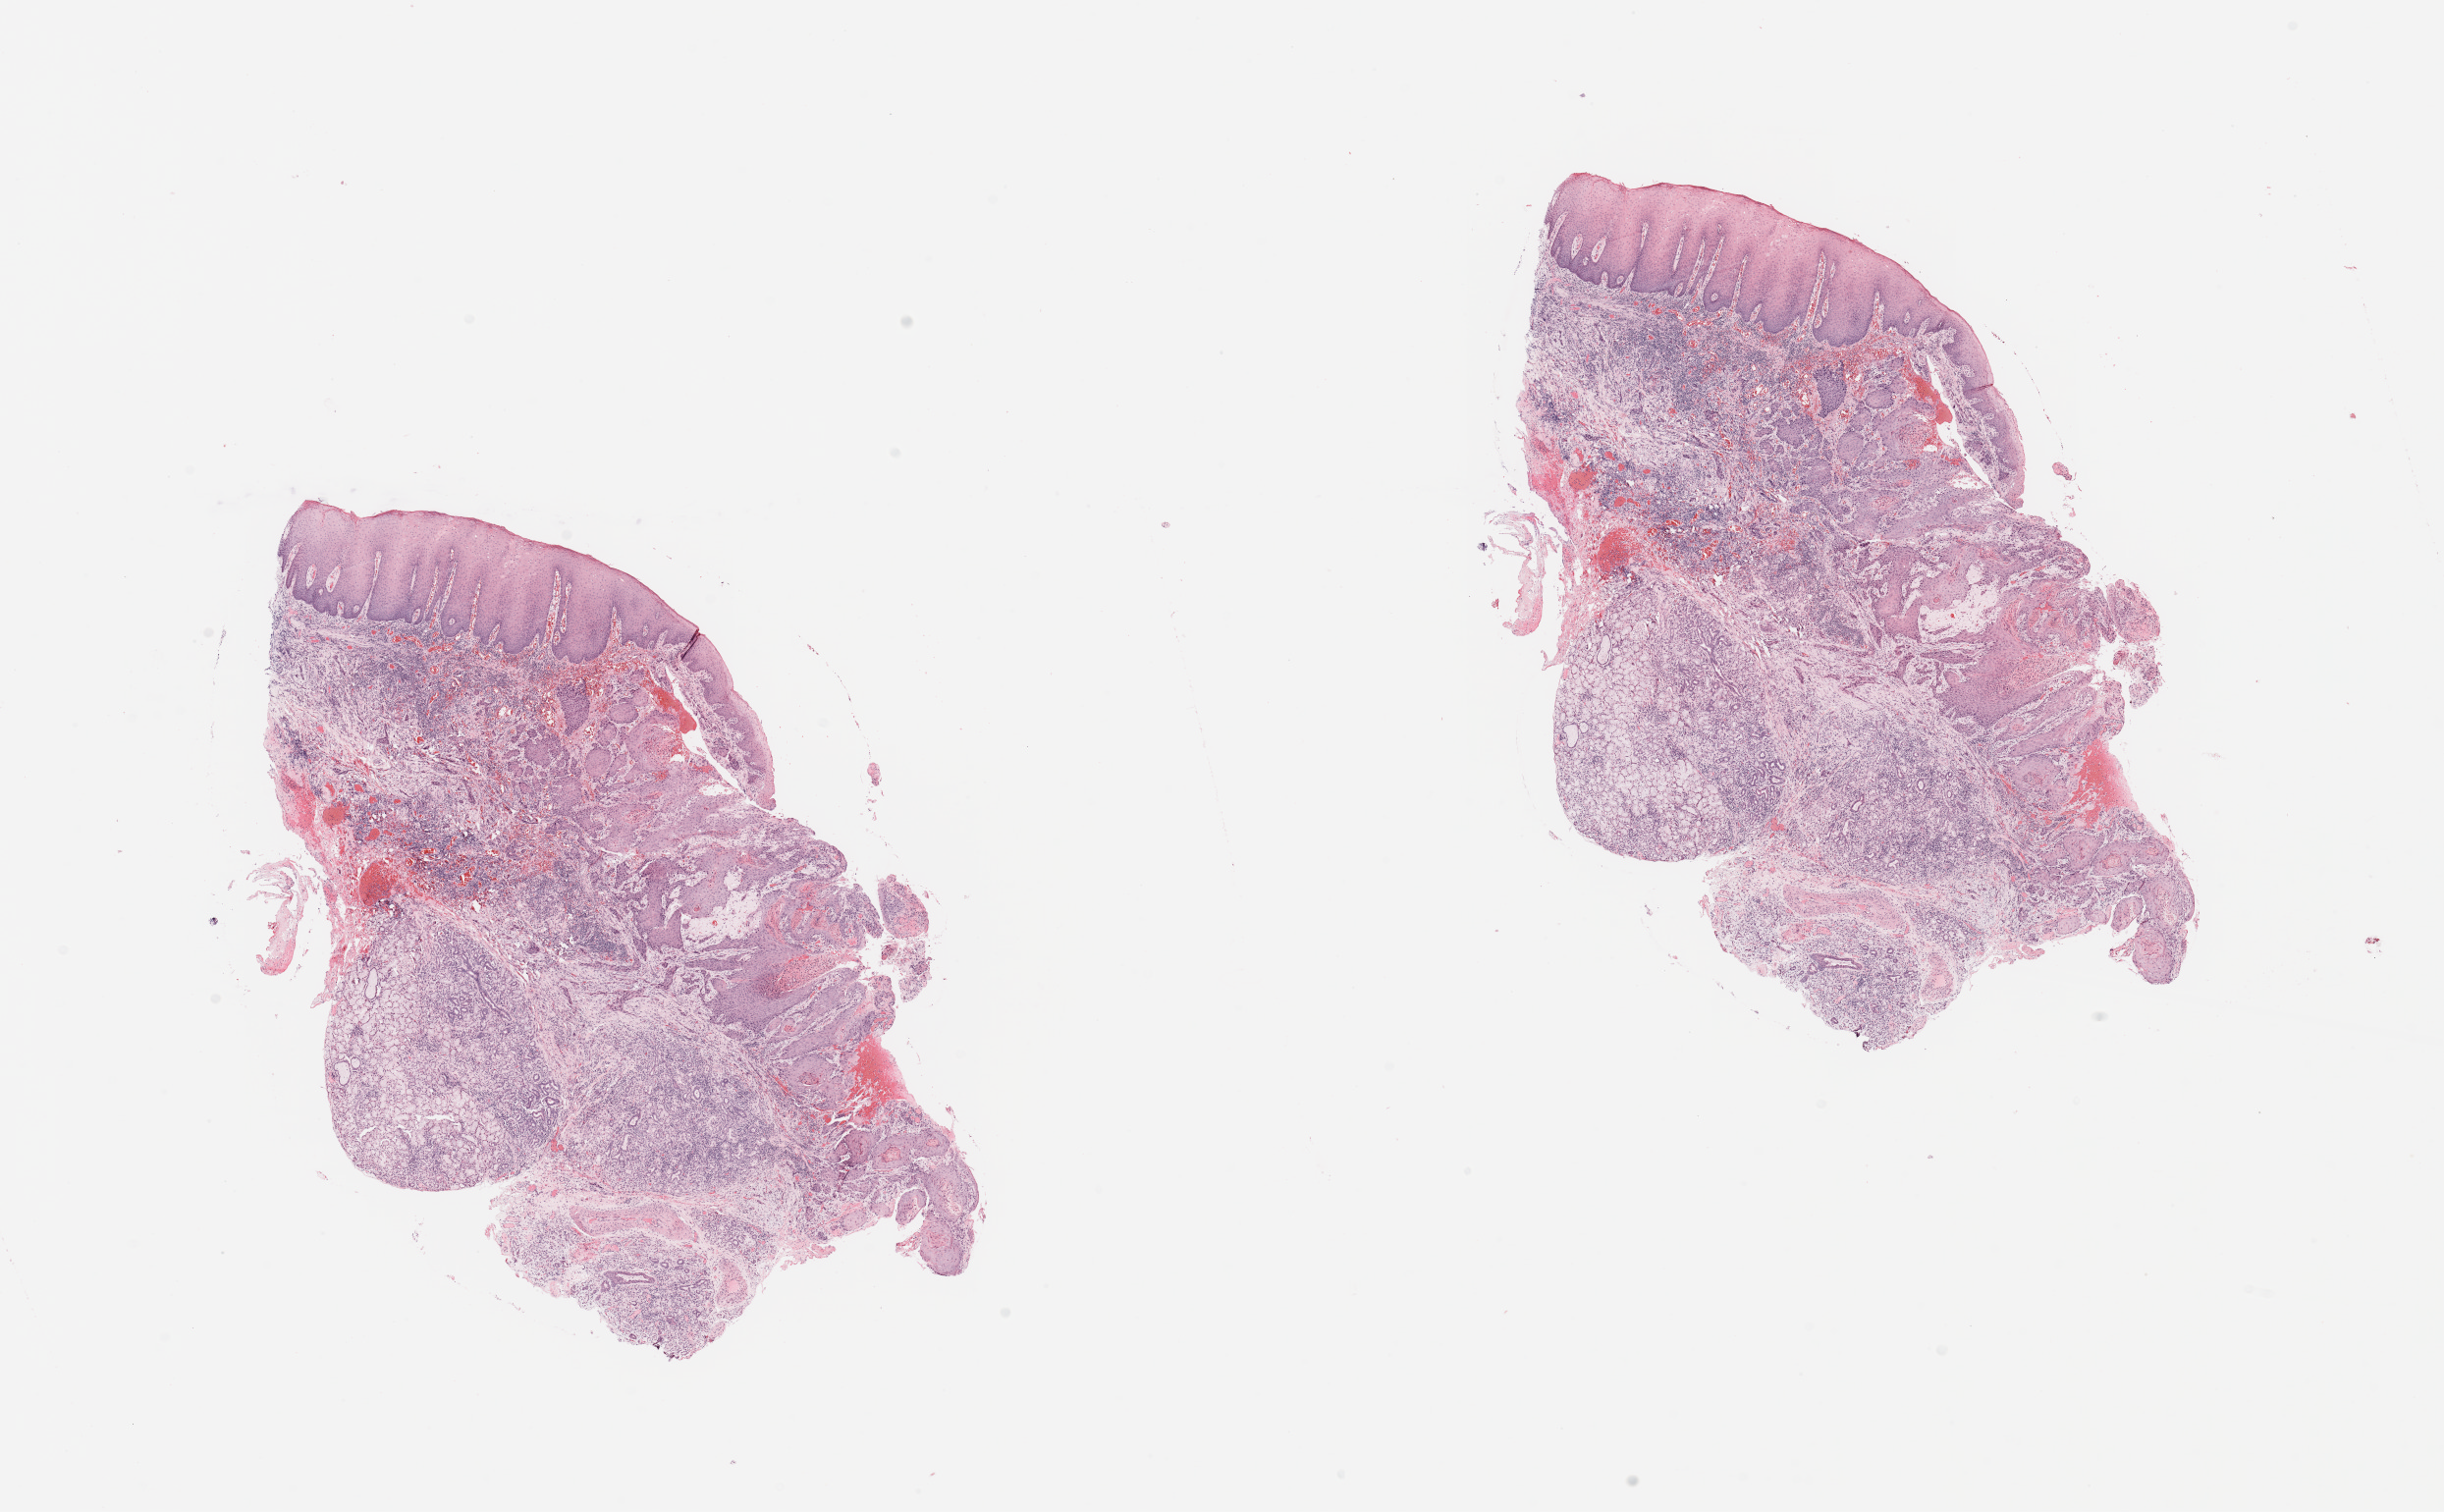
Digitized H&E-stained tissue section (whole slide), a low-resolution overview of the entire scanned area, about 19.7 x 12.2 mm; head and neck, tissue type not recorded. 67-year-old female patient.
Patient diagnosis: Squamous cell carcinoma, NOS (overlapping lesion of lip, oral cavity and pharynx).